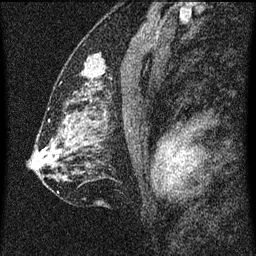
Breast MRI (dynamic contrast-enhanced), one sagittal slice. Position 39 of 60 along the scan axis. Dynamic contrast-enhanced series, image 2 of 3 at this slice position (ordered by acquisition). 1.5 T. TE 4.2 ms, TR 8 ms. 2 mm slice thickness. 256 × 256 image matrix, field of view 180 × 180 mm. Patient: female, 52 years.
Structures marked on this image (semi-automatic segmentation, software-assisted and operator-edited):
- analysis volume of interest (the breast-tissue region the enhancement analysis was run in; not a lesion): bounding box <72,50,116,101> (left, top, right, bottom; pixels)
- tumour enhancement mask (voxels above the 70 % enhancement threshold inside the analysis volume of interest): <83,62,89,75>